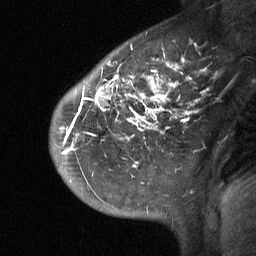
Breast MRI (dynamic contrast-enhanced), one sagittal slice; position 44 of 64 along the scan axis; dynamic contrast-enhanced study with each time point stored as its own series, time point 2 of 3 at this slice position (early post-contrast, ordered by acquisition time); 1.5 T; TE 4.8 ms, TR 27 ms; 2 mm slice thickness; 256 × 256 image matrix, field of view 200 × 200 mm. Patient: female, 42 years. From the clinical record (not read from this slice): setting: breast cancer imaged before/during neoadjuvant chemotherapy; receptor status: triple-negative.
Outlined on this slice (semi-automatically segmented with operator editing):
- analysis volume of interest (the breast-tissue region the enhancement analysis was run in; not a lesion): bounding box (x1, y1, x2, y2) in pixels: (50, 29, 198, 190)
- tumour enhancement mask (voxels above the 90 % enhancement threshold inside the analysis volume of interest): (62, 58, 191, 154)